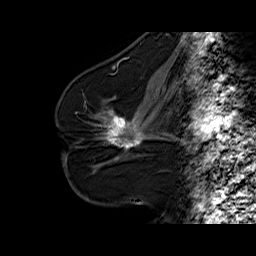
Breast MRI (dynamic contrast-enhanced), one sagittal slice; dynamic contrast-enhanced series, time point 2 of 6 at this slice position (early post-contrast); 1.5 T; TE 6.3 ms, TR 32.5 ms; 4 mm slice thickness; 256 × 256 image matrix. Female patient. From the clinical record (not read from this slice): setting: breast cancer imaged before/during neoadjuvant chemotherapy; receptor status: HR-positive, HER2-negative.
Outlined on this slice (semi-automatic segmentation, software-assisted and operator-edited):
- analysis volume of interest (the breast-tissue region the enhancement analysis was run in; not a lesion): bounding box <94,103,161,164> (left, top, right, bottom; pixels)
- tumour enhancement mask (voxels above the 100 % enhancement threshold inside the analysis volume of interest): <107,111,140,149>